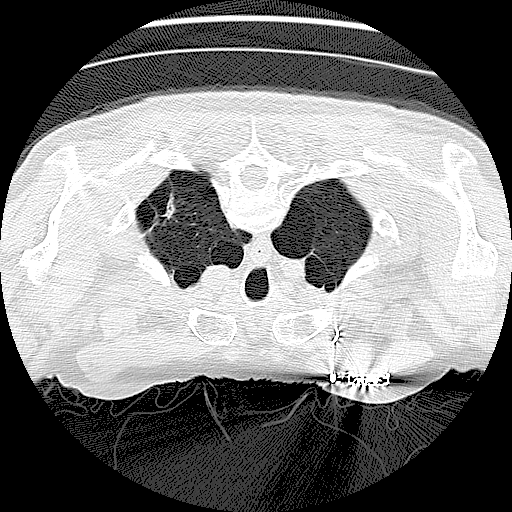
Axial slice from a low-dose chest CT screening exam. Baseline annual screen. Lung window (W 1500 / L -600 HU). 2.5 mm slice thickness. Lung (sharp) reconstruction kernel (LUNG). Slice 18 of 138 in the series. Male, age 73 years at enrolment. Current smoker at enrolment.
Expert reader's lesion annotation, bounding box <144,187,189,237> (left, top, right, bottom; pixels). The screening reader recorded 2 non-calcified nodules or masses ≥4 mm on this exam (left lower lobe, right middle lobe); which of them this box marks is not recorded. Participant outcome: lung cancer diagnosed 308 days after this screen — neoplasm, malignant, stage IV (AJCC 6th edition).